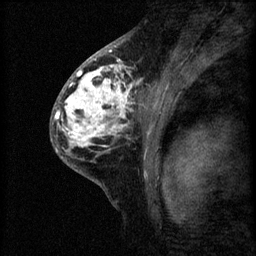
Breast MRI (dynamic contrast-enhanced), one sagittal slice; position 36 of 60 along the scan axis; 3 images stored at this slice position (order not interpretable as contrast timing); 1.5 T; TE 4.2 ms, TR 8.2 ms; 2 mm slice thickness; 256 × 256 image matrix, field of view 180 × 180 mm. Patient: female, 41 years.
Structures marked on this image (semi-automatic segmentation, software-assisted and operator-edited):
- analysis volume of interest (the breast-tissue region the enhancement analysis was run in; not a lesion): bounding box <53,62,160,175> (left, top, right, bottom; pixels)
- tumour enhancement mask (voxels above the 70 % enhancement threshold inside the analysis volume of interest): <54,62,139,147>